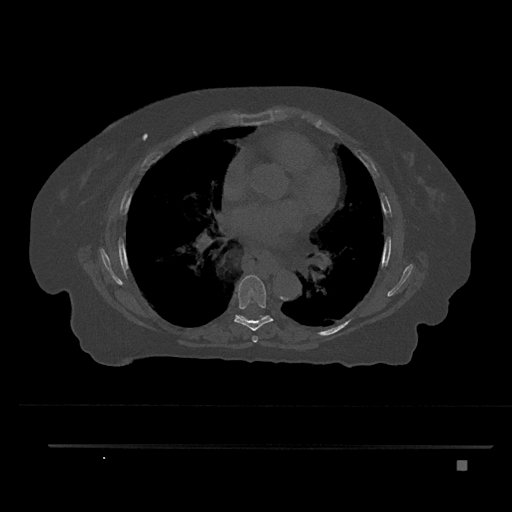
CT including the spine, one axial slice; slice 484 of 797 in the series (ordered by position); bone window (W 1800 / L 400 HU); 0.5 mm slice thickness; 512 × 512 image matrix, field of view 437 × 437 mm. Patient: female, 76 years. Case-level facts recorded for this patient, not image findings: primary cancer: lung.
Structures marked on this image (semi-automatic segmentation, software-assisted and operator-edited):
- T6 vertebra: bounding box [x1, y1, x2, y2] px = [252, 336, 258, 343]
- T7 vertebra: [234, 275, 274, 331]
- T8 vertebra: [236, 315, 269, 320]